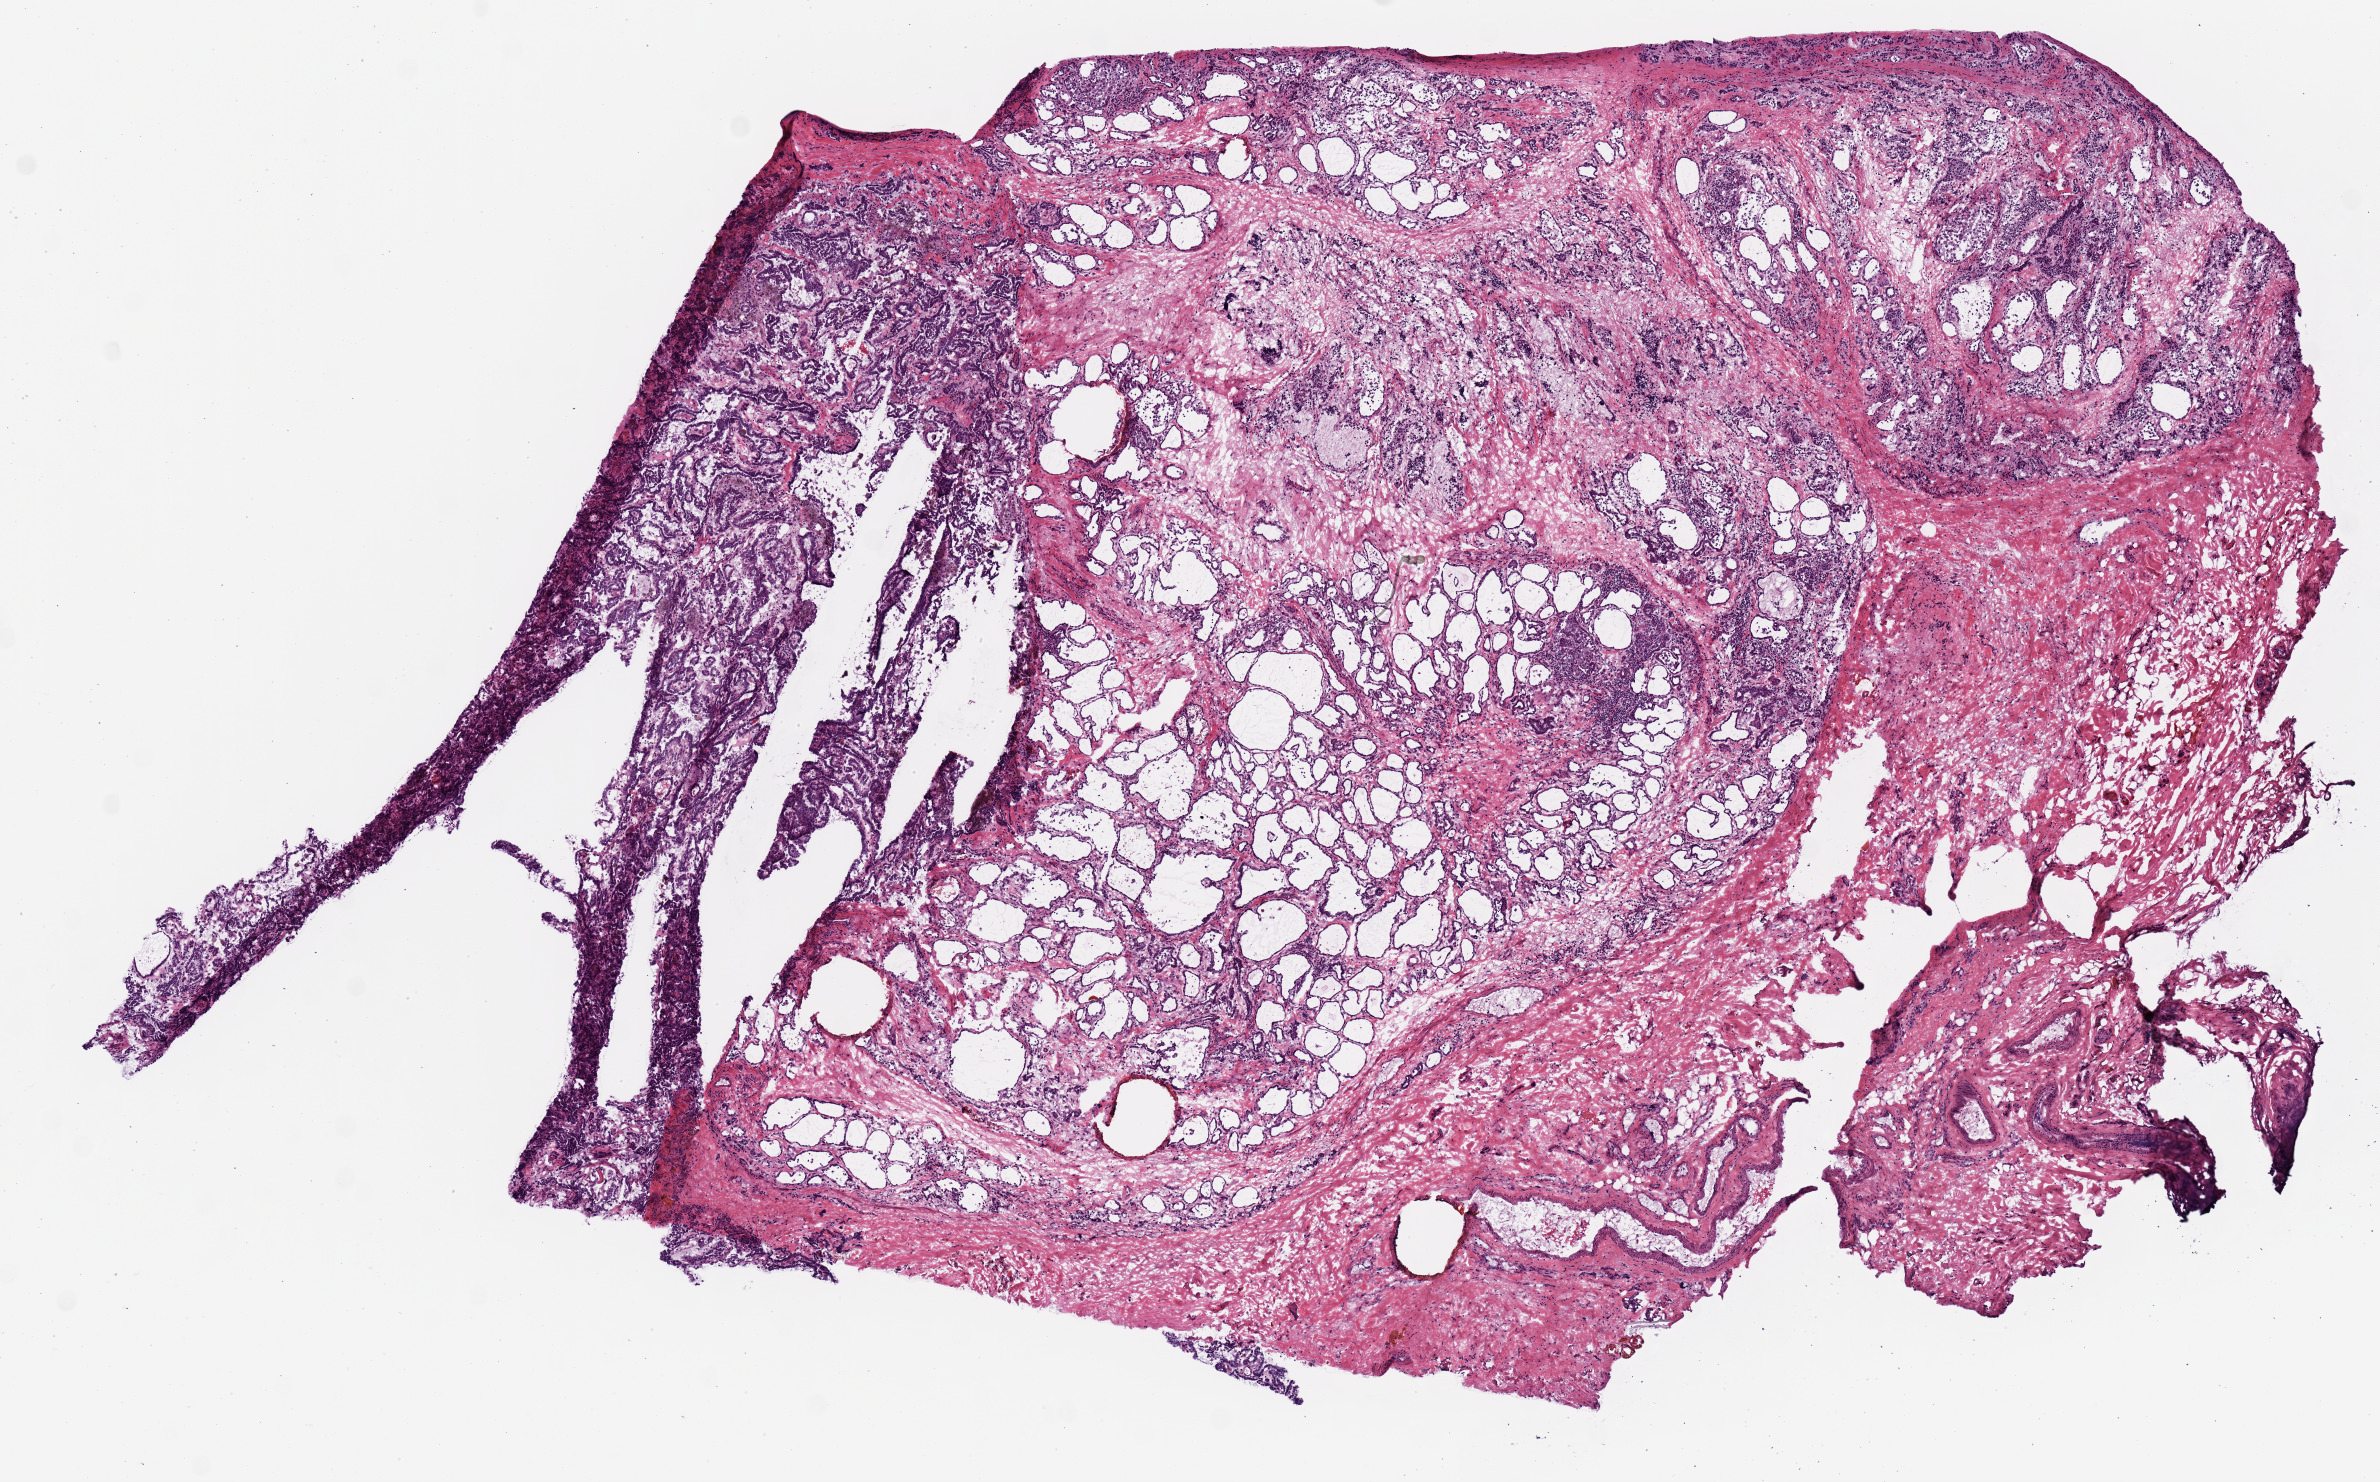
Digitized Hematoxylin and eosin (H&E) stained tissue section (whole slide), whole scanned area (about 9.4 x 5.9 mm, slide scanned at 20x) shown as a low-resolution overview. Frozen section from the top of the tissue portion. Sample: primary tumour, thyroid. Female patient; age at initial diagnosis 46 years. Pathologist review of this section (percent, as recorded): tumour cells 85%, tumour nuclei 85%, normal cells 0%, stromal cells 15%, necrosis 0%. Infiltration values recorded for this section: lymphocyte infiltration 0%, monocyte infiltration 0%, neutrophil infiltration 0%.
Pathologic diagnosis: Papillary adenocarcinoma, NOS (thyroid gland). AJCC pathologic stage: I (7th edition).